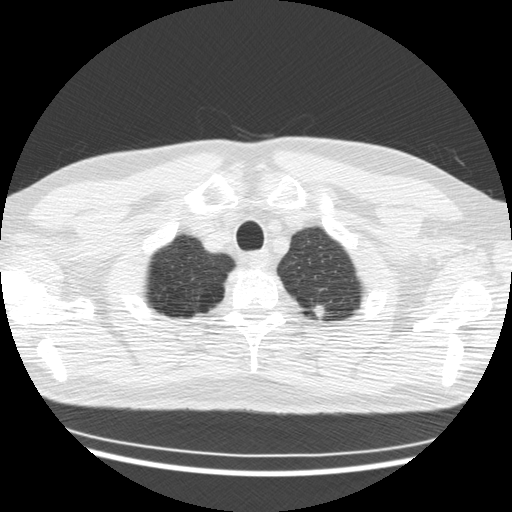
Low-dose screening chest CT, axial slice. Second annual screen. Lung window (W 1500 / L -600 HU). 2.5 mm slice thickness. Standard (soft-tissue) reconstruction kernel (STANDARD). Slice 20 of 176 in the series. 512 × 512 image matrix. Male participant, aged 57 years at enrolment. Former smoker at enrolment.
Lesion marked by an expert reader, bounding box [x1, y1, x2, y2] px = [305, 298, 335, 324]. The screening reader recorded 2 non-calcified nodules or masses ≥4 mm on this exam; which of them this box marks is not recorded. Lung cancer was diagnosed 332 days after this screen: adenocarcinoma, NOS, left upper lobe, stage IV (AJCC 6th edition), 50 mm at pathology.